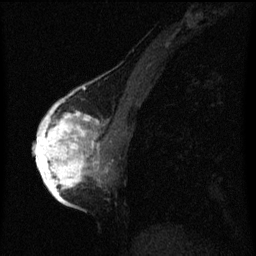
Breast MRI (dynamic contrast-enhanced), one sagittal slice; position 27 of 60 along the scan axis; dynamic contrast-enhanced series, image 2 of 3 at this slice position (ordered by acquisition); 1.5 T; TE 4.2 ms, TR 8 ms; 256 × 256 image matrix, field of view 180 × 180 mm. Patient: female, 56 years.
Structures marked on this image (semi-automatically segmented with operator editing):
- analysis volume of interest (the breast-tissue region the enhancement analysis was run in; not a lesion): bounding box [x1, y1, x2, y2] px = [42, 110, 107, 193]
- tumour enhancement mask (voxels above the 70 % enhancement threshold inside the analysis volume of interest): [42, 110, 99, 193]